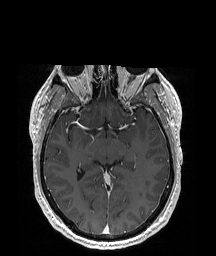
Brain MRI from a brain-tumour surgery series, one axial slice. Position 111 of 192 along the scan axis. T1-weighted post-contrast. 1 mm slice thickness. 216 × 256 image matrix, field of view 219 × 260 mm. From the clinical record (not read from this slice): histopathology: Glioblastoma; WHO grade: 4; IDH mutation: no; tumour location: Left Temporal Parietal.
Structures marked on this image (expert manual segmentation):
- tumour: bounding box [x1, y1, x2, y2] px = [153, 177, 161, 196]